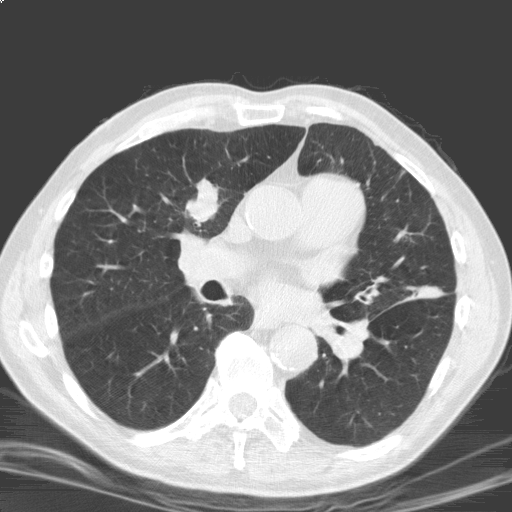
Axial slice from a low-dose chest CT screening exam, second screening round (one year after baseline), lung window (W 1500 / L -600 HU), standard (soft-tissue) reconstruction kernel (C). Male, age 69 years at enrolment.
- Lesion marked by an expert reader, bounding box (x1, y1, x2, y2) in pixels: (172, 173, 231, 230).
- The screening reader recorded 2 non-calcified nodules or masses ≥4 mm on this exam; which of them this box marks is not recorded.